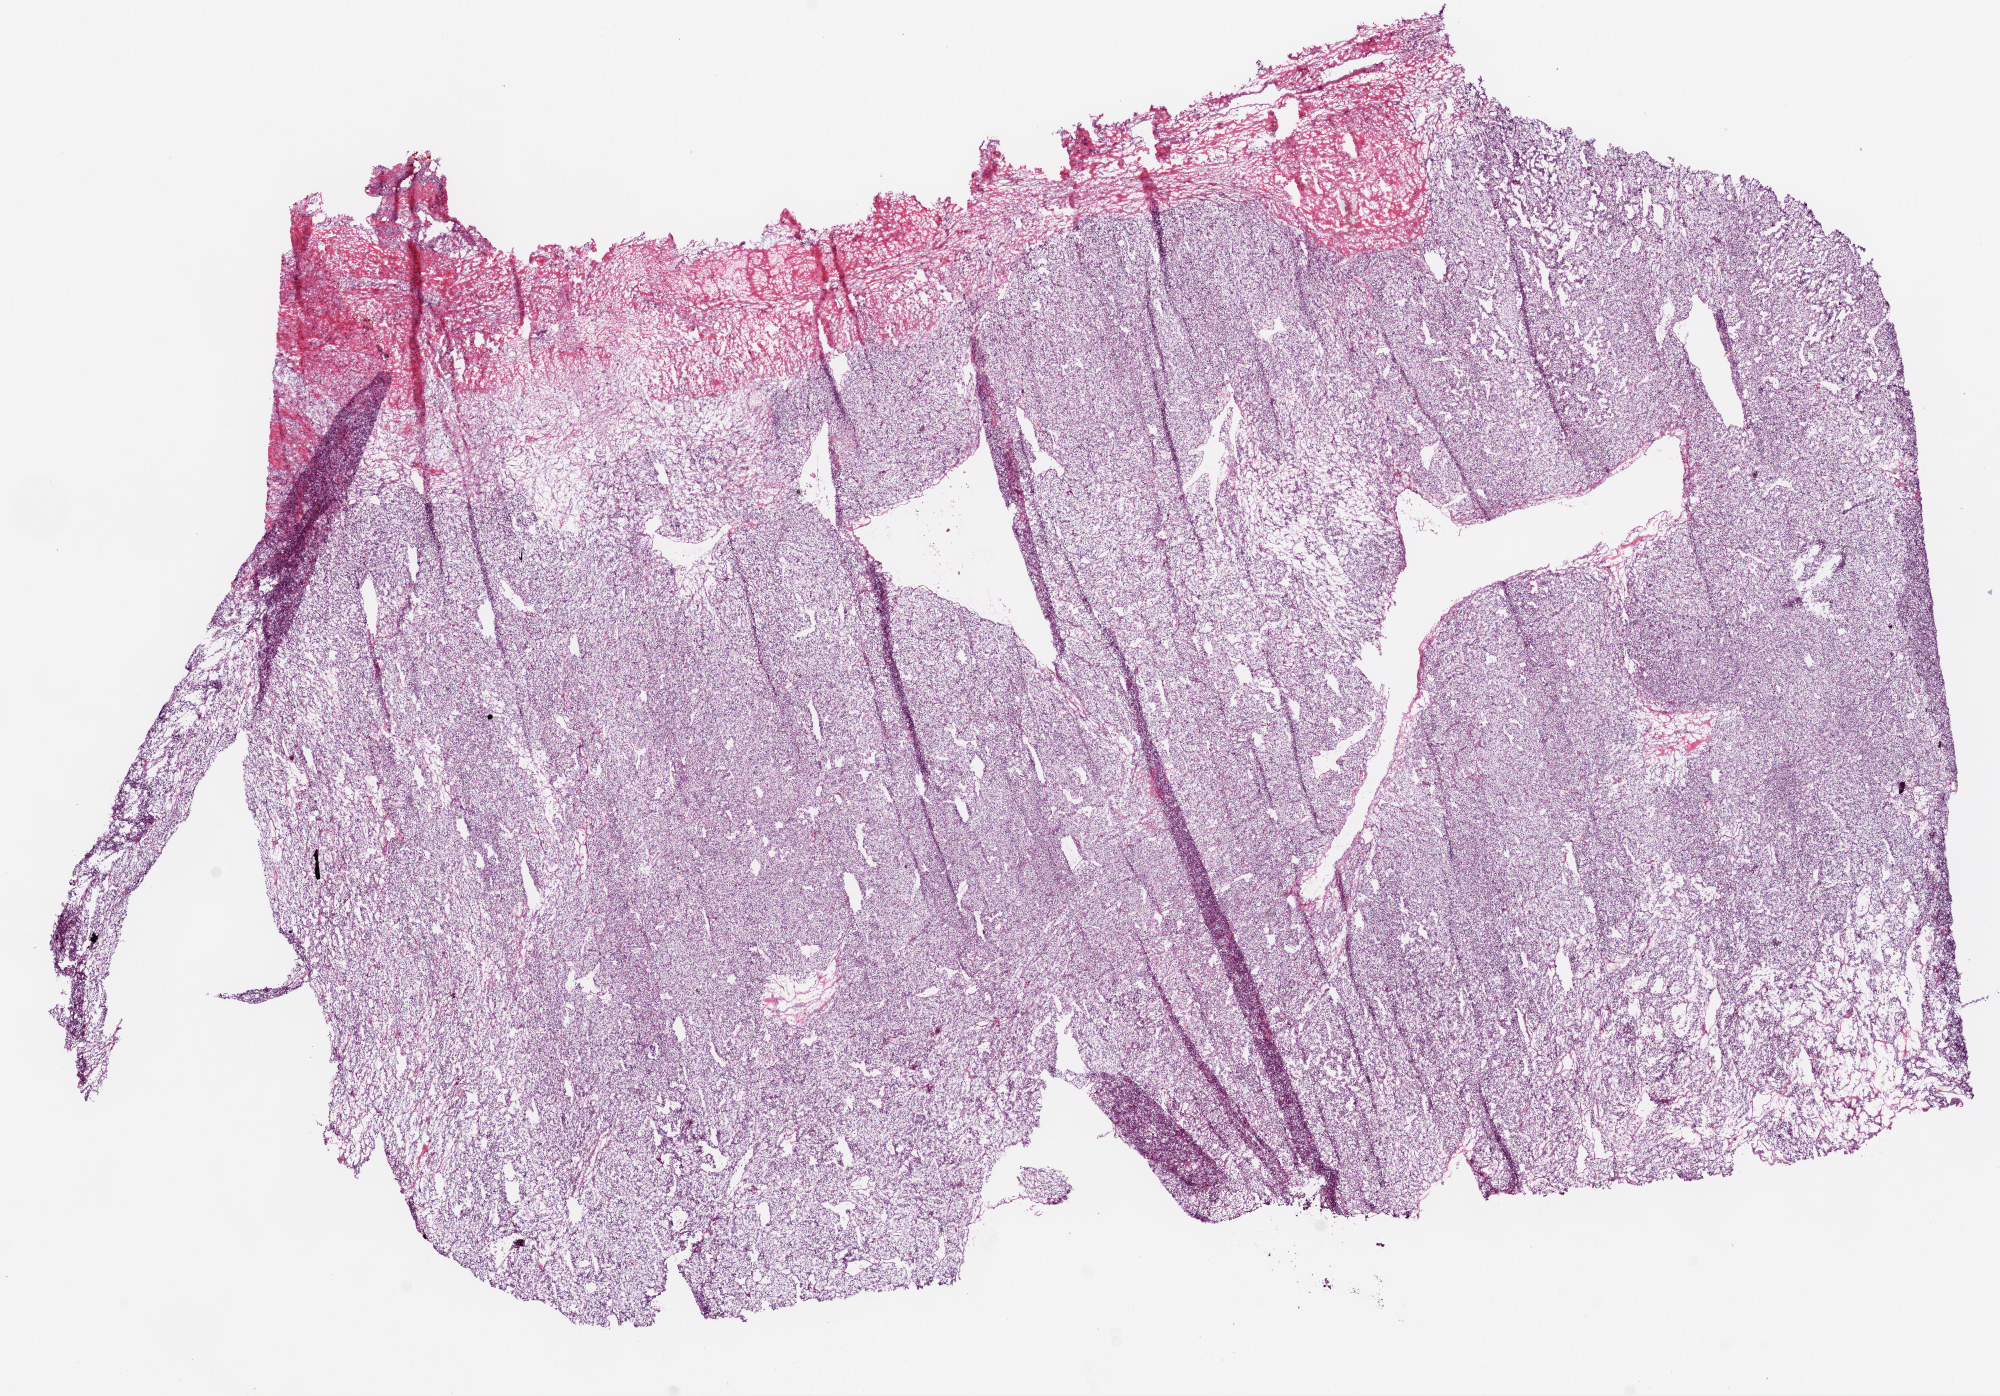
Digitized H&E tissue section (whole slide), whole scanned area (about 16.0 x 11.2 mm) shown as a low-resolution overview. Frozen section. Sample: primary tumour, kidney. Male, age 42 years at initial diagnosis. Histologic grade: G2 (moderately differentiated). Slide review estimates, as recorded: tumour cells 85%, tumour nuclei 70%, normal cells 0%, stromal cells 15%, necrosis 0%.
Histologic diagnosis: Clear cell adenocarcinoma, NOS. AJCC pathologic stage: II.